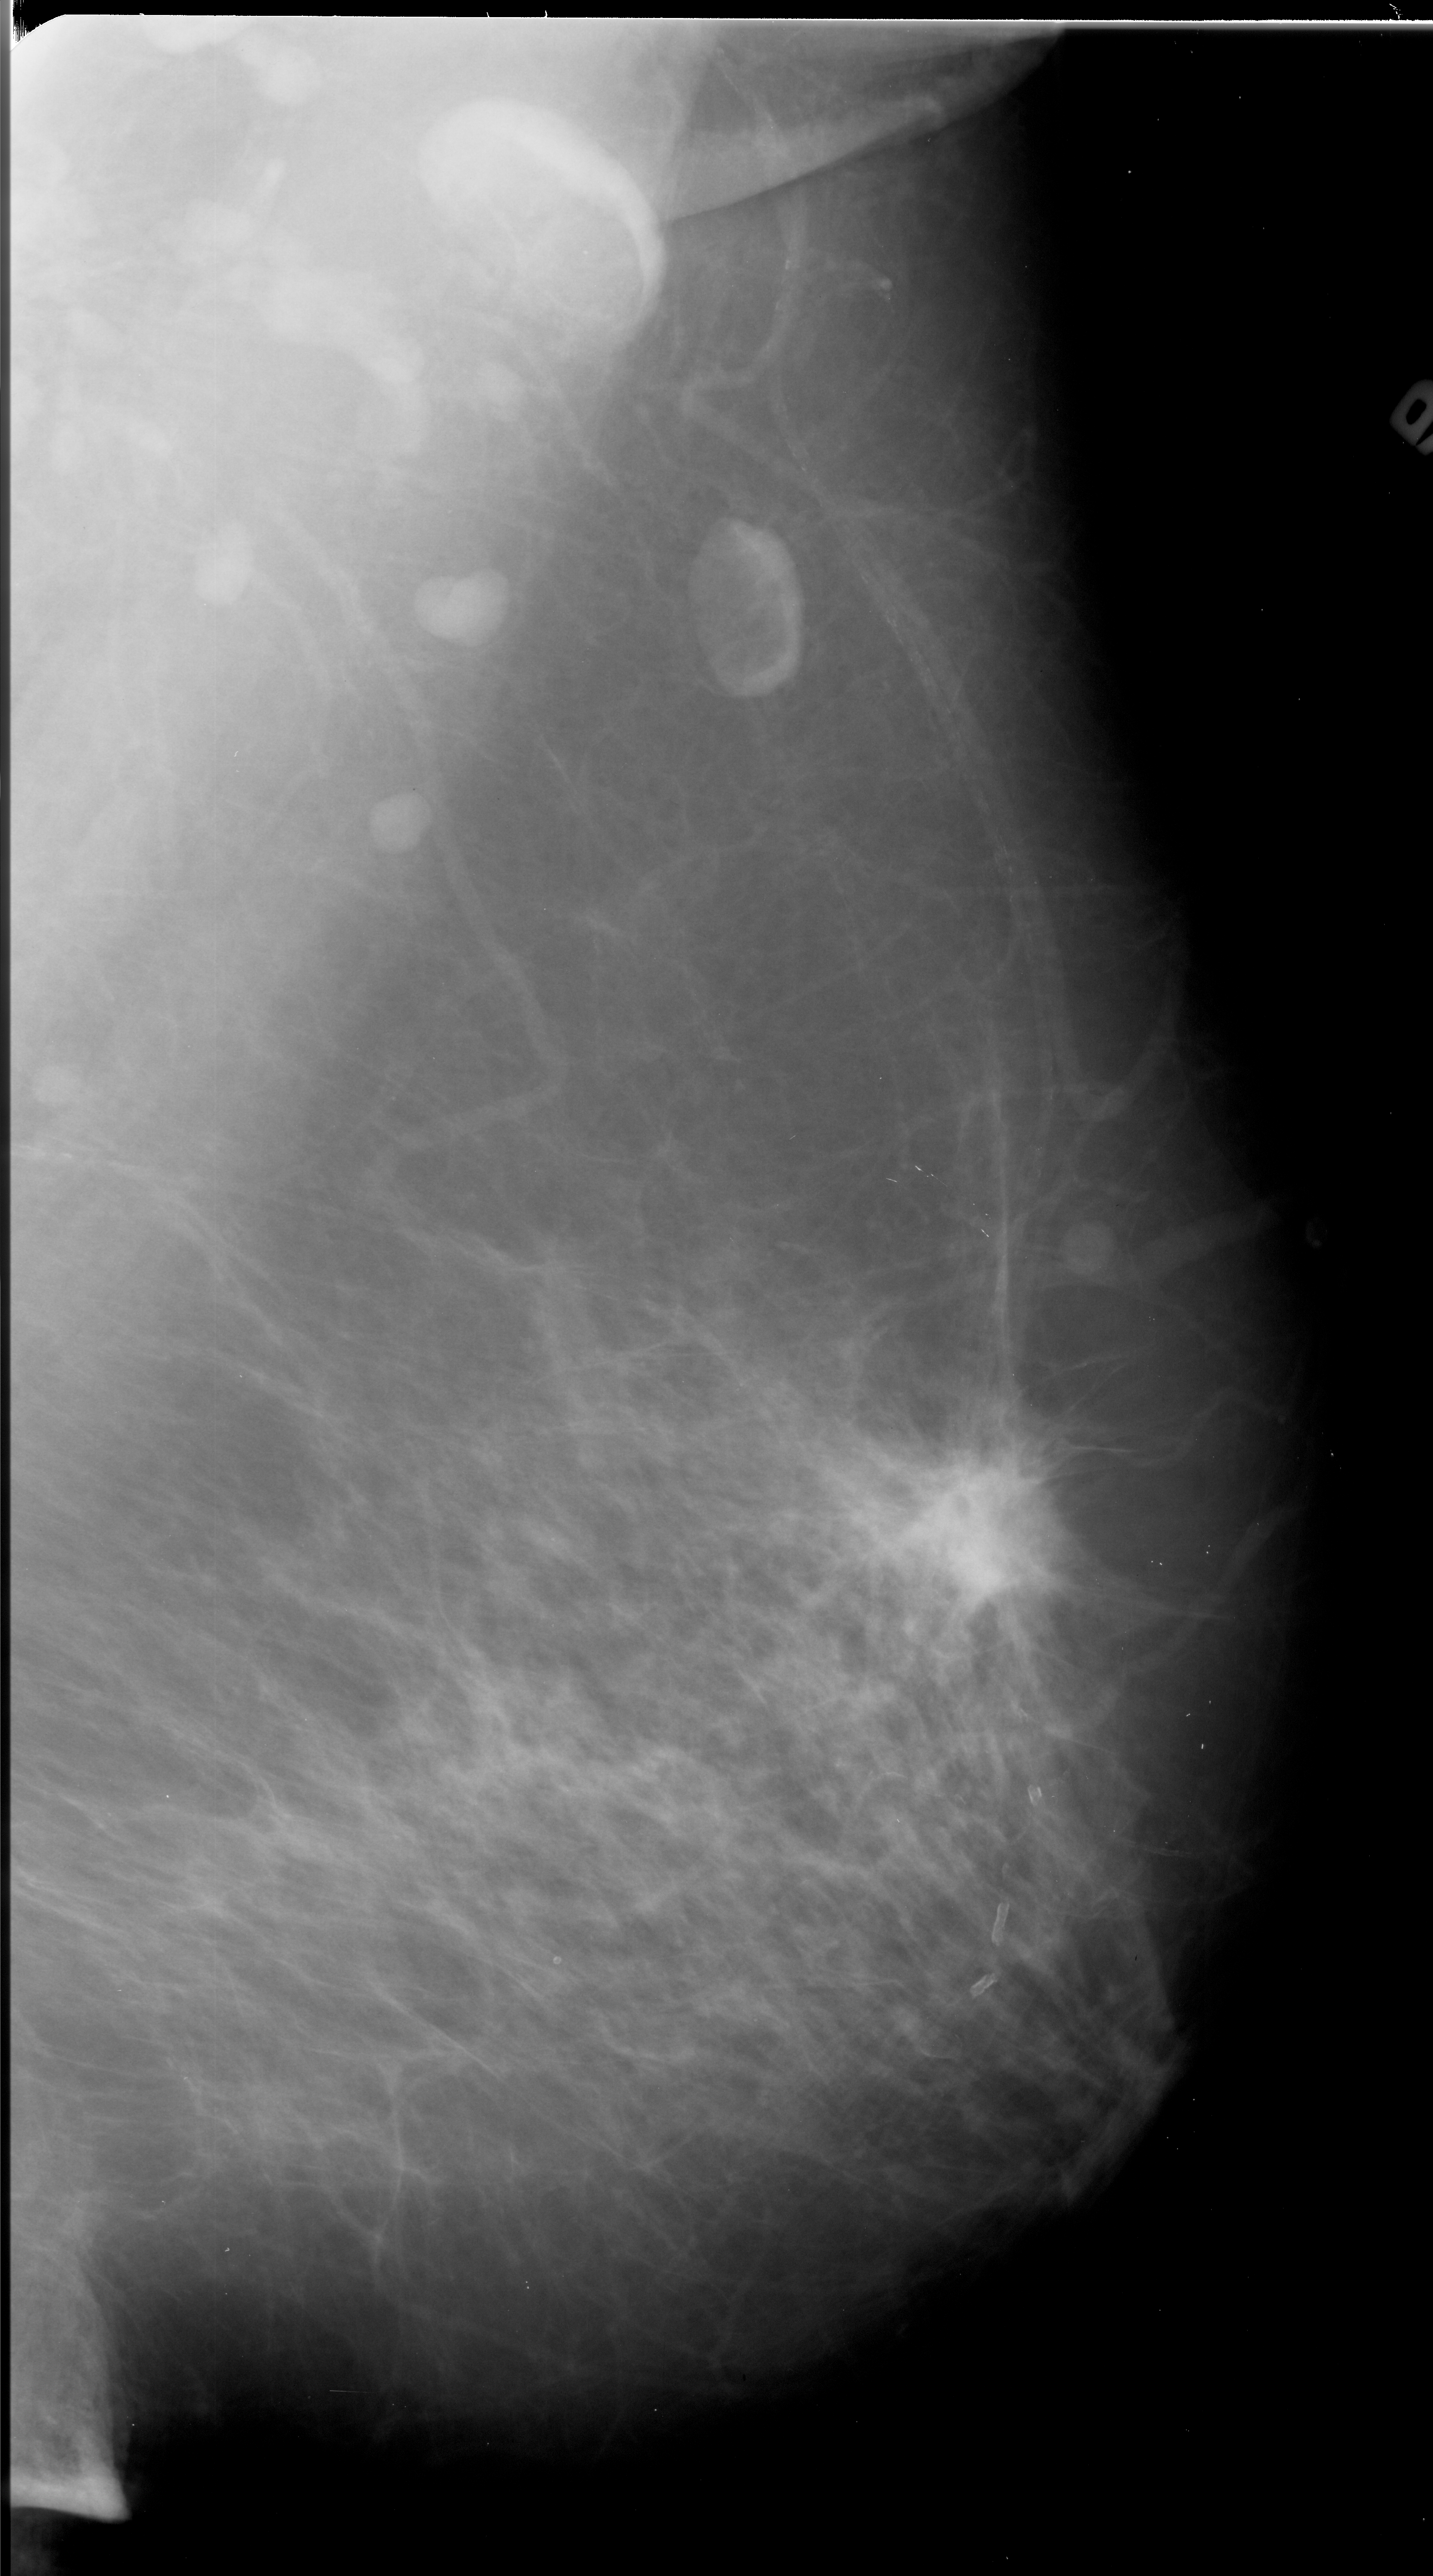
Mammogram (digitized film); right breast; MLO view; BI-RADS breast density category 2 (scale 1–4); 1433 × 2576 image matrix.
Marked abnormalities (boxes around the expert regions of interest):
- mass, shape irregular, margins spiculated; BI-RADS assessment category 5; pathology (as recorded): malignant: bounding box (x1, y1, x2, y2) in pixels: (867, 1446, 1085, 1634)